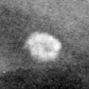
Cropped region of a digitized screen-film mammogram centred on a radiologist-marked abnormality, left breast, CC view, BI-RADS breast density category 3 (scale 1–4).
Calcifications, morphology lucent center; BI-RADS assessment category 2; subtlety rating 4 on a 1 (subtle) to 5 (obvious) scale; benign without callback (not worked up further).